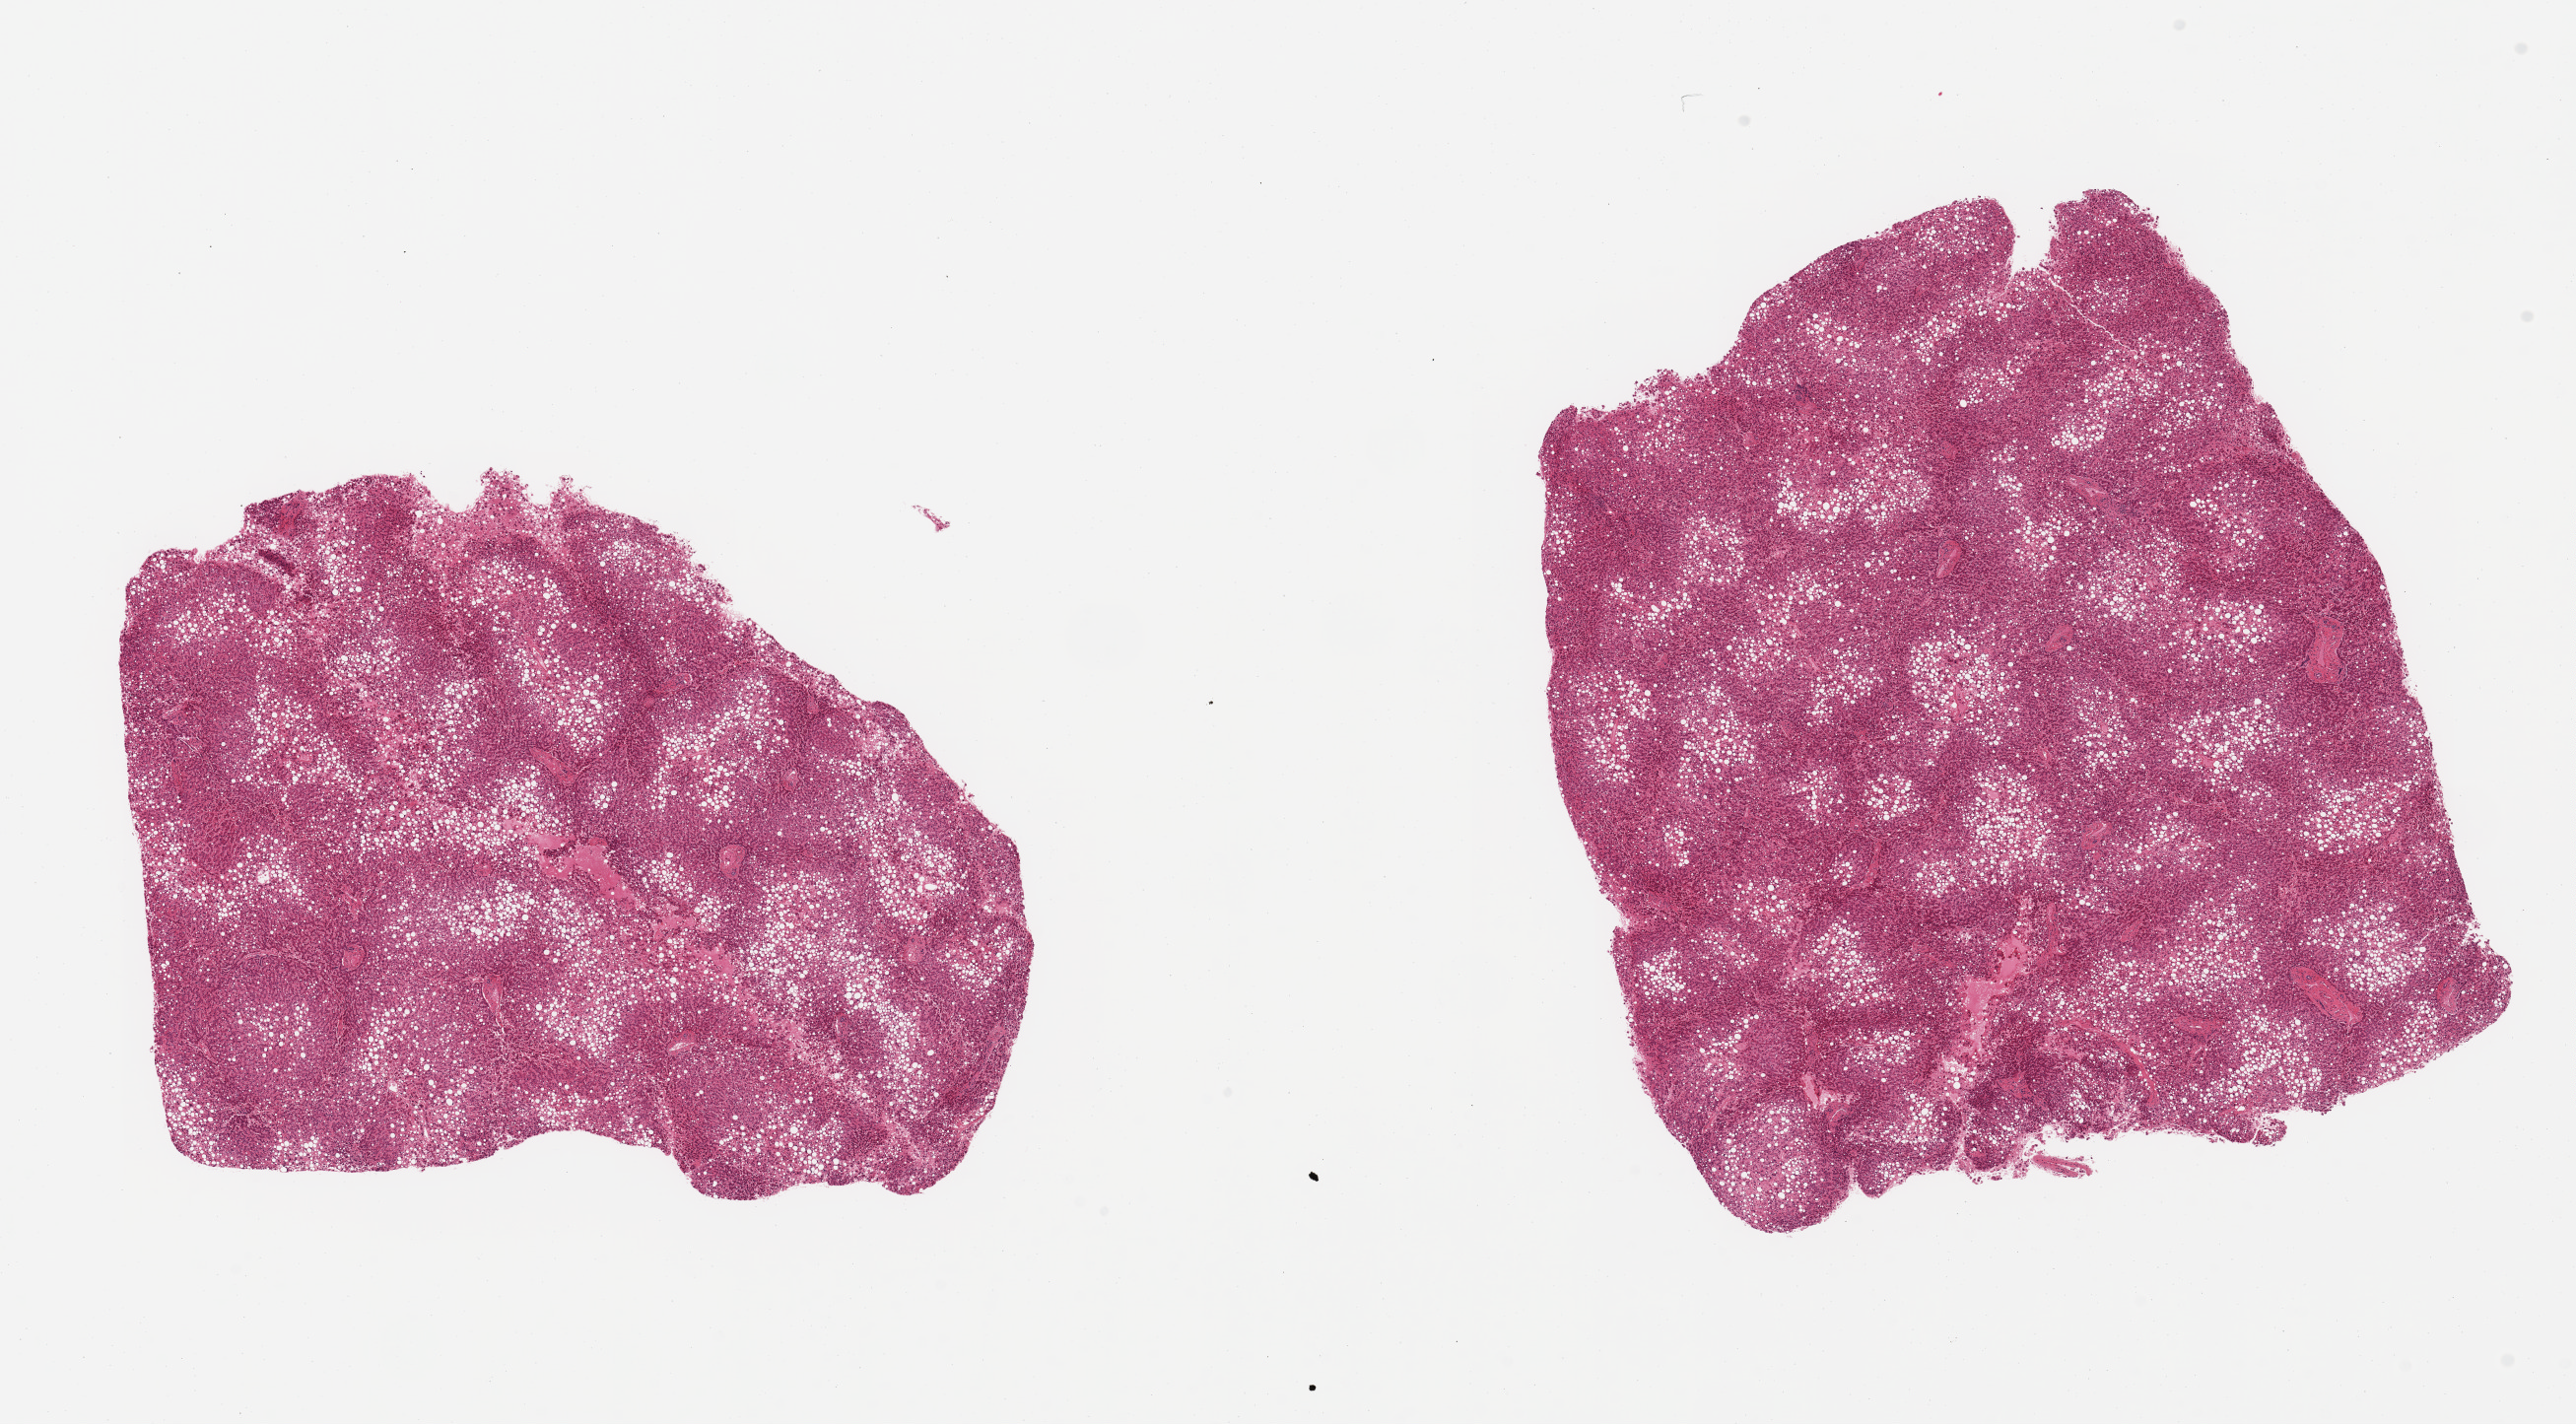
Whole-slide image, hematoxylin and eosin (H&E) stain, low-resolution overview of the scanned area, about 20.7 x 11.4 mm (slide scanned at 20x), PAXgene-fixed, paraffin-embedded tissue, target tissue: liver, donor tissue sample. Donor sex: female.
Pathologist's review note for this sample: 2 pieces; severe central macrovesicular steatosis.